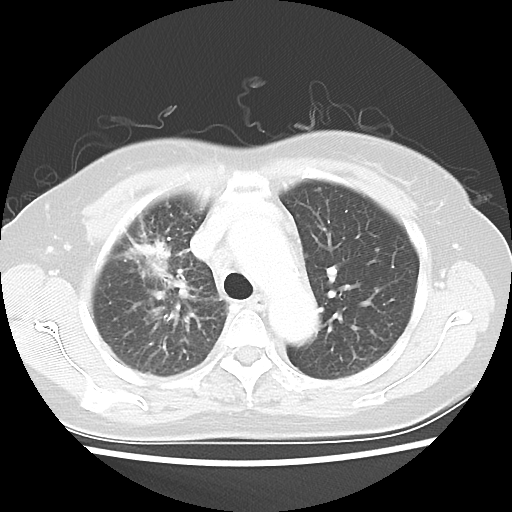
Chest CT, one axial slice; slice 33 of 48 in the series (ordered by position); reconstruction kernel LUNG; 100 kVp; lung window (W 1500 / L -600 HU); 5 mm slice thickness; 512 × 512 image matrix. Patient: female, 55 years. From the clinical record (not read from this slice): clinical TNM (as recorded): T1b N3 M1a.
Outlined on this slice (rectangle marked by the reading radiologist):
- lung tumour (recorded histology: adenocarcinoma): bounding box (x1, y1, x2, y2) in pixels: (124, 232, 172, 278)